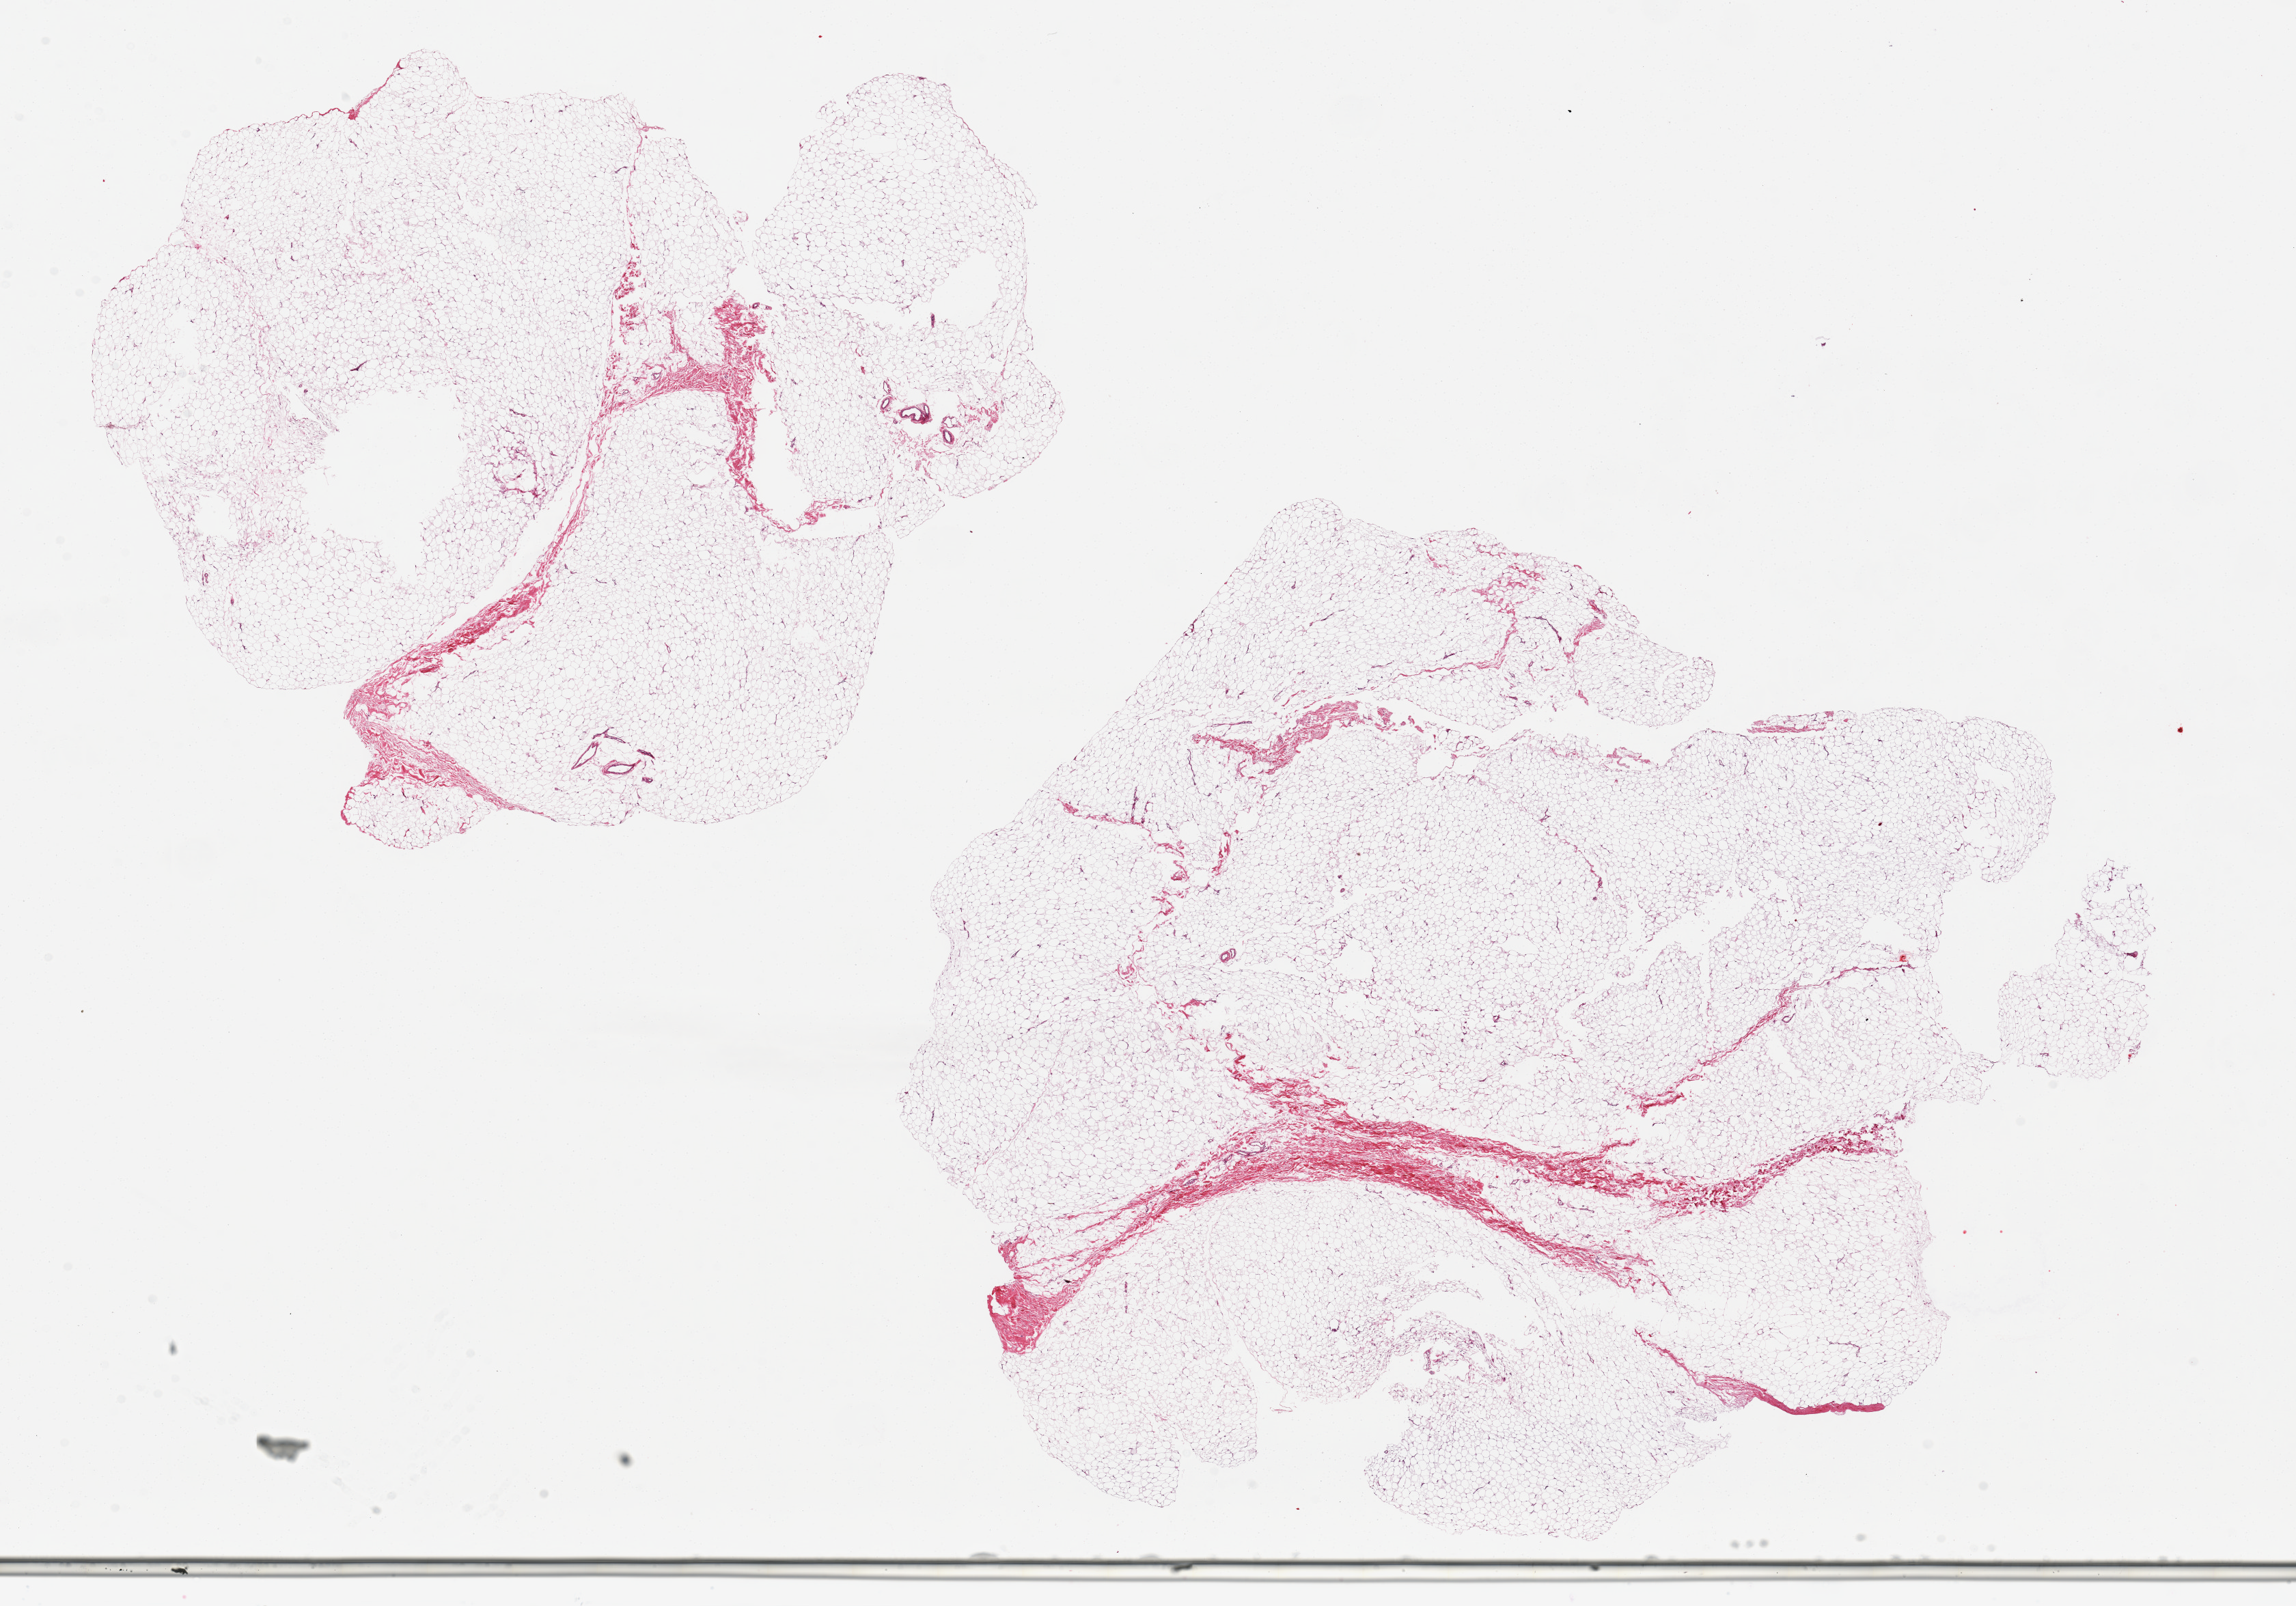
Digitized H&E-stained section, low-resolution overview of the scanned area, about 26.6 x 18.6 mm; PAXgene-fixed paraffin-embedded (PFPE) section; sampled site (target tissue): breast; tissue donor sample. Donor sex: male.
Pathologist's review note for this sample: 2 aliquots, ~9x9mm. All fibroadipose tissue; no ductal elements noted.